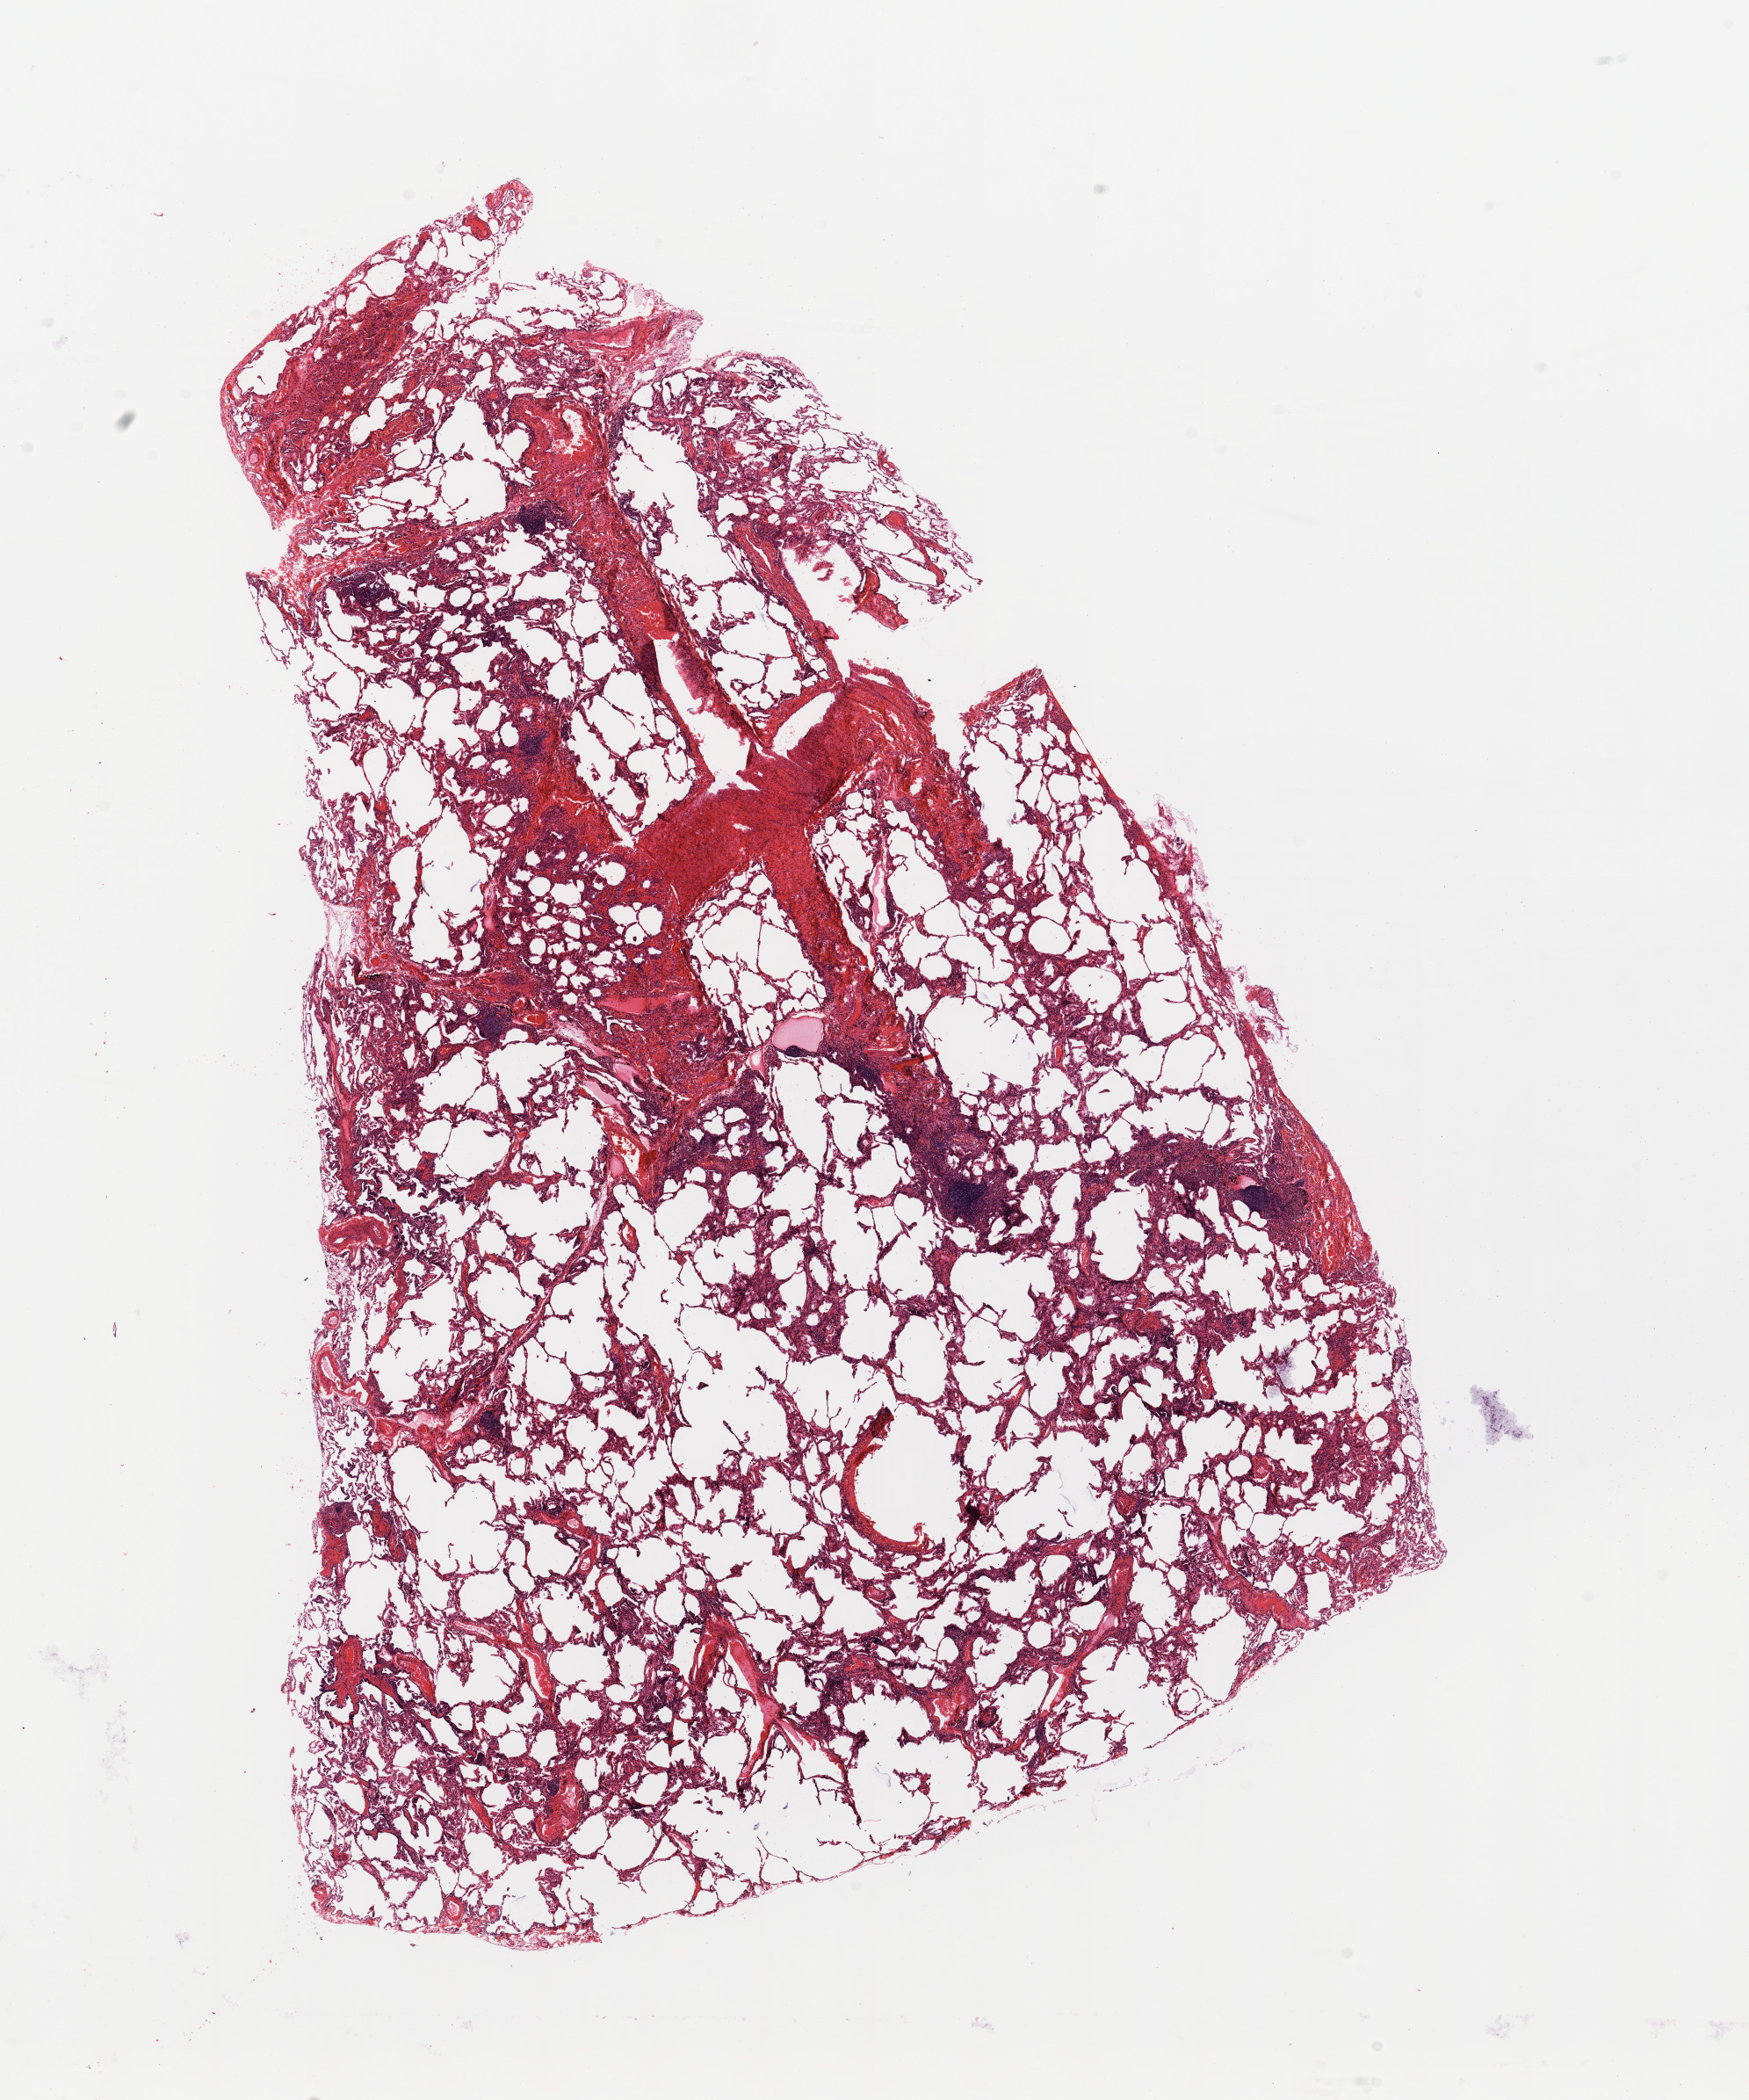
Digitized H&E-stained tissue section (whole slide), shown as a low-resolution overview of the whole scanned area (about 15.8 x 18.9 mm). Normal (non-tumour) tissue sample, sampled site: lung. Patient: male, age 56 years.
This section: normal (non-tumour) tissue from the same patient. Patient diagnosis: Adenocarcinoma, NOS.